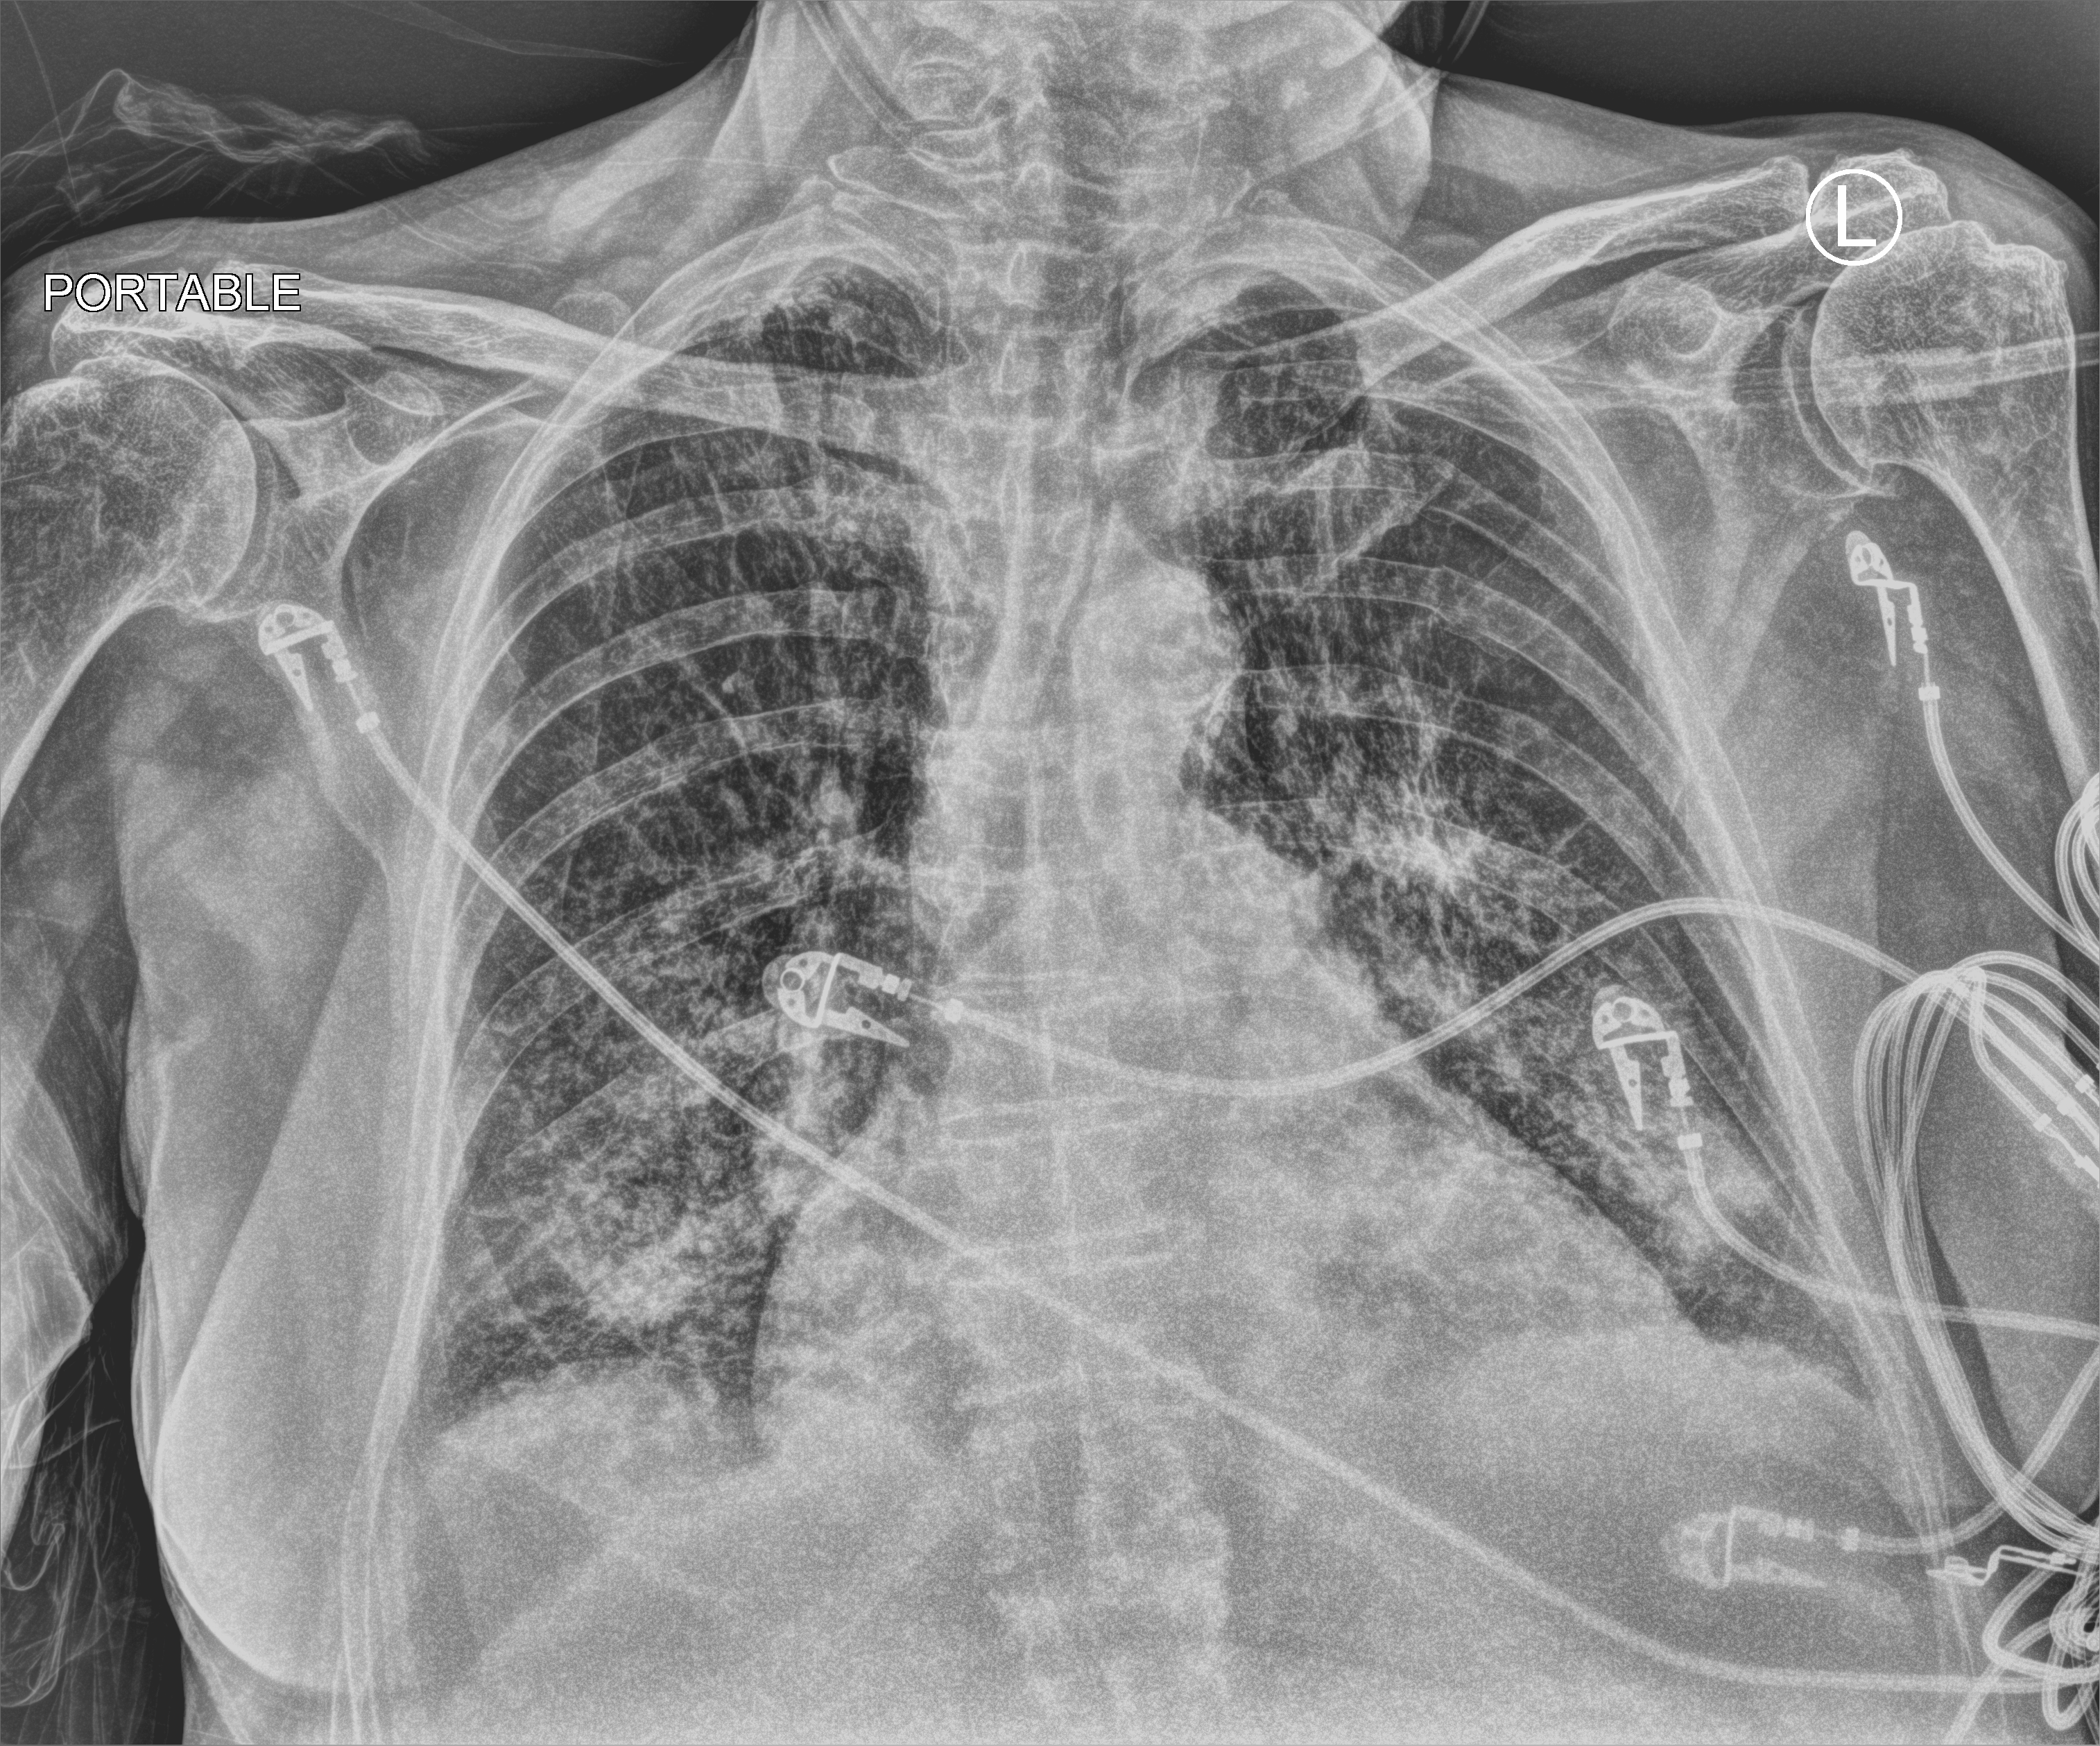
Chest X-ray (portable). Patient hospitalised with COVID-19; male, aged 75–90 years.
Admission-level facts for this patient (not findings on this image; timing relative to this image not recorded):
- admitted to intensive care during this hospital stay: no
- hypertension (admission record): yes
- smoking status (admission record): former